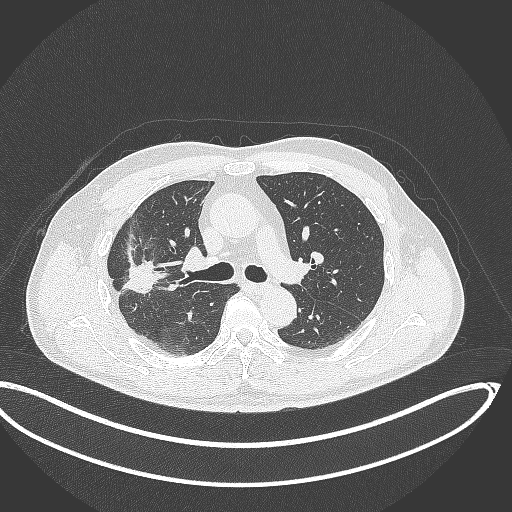
Chest CT, one axial slice. Position 217 of 391 along the scan axis. 120 kVp. Lung window (W 1500 / L -600 HU). 1 mm slice thickness. 512 × 512 image matrix, field of view 439 × 439 mm. Patient: male, 63 years. From the clinical record (not read from this slice): clinical TNM (as recorded): T1c N0 M0; histopathological grade: G2-3.
Structures marked on this image (rectangle marked by the reading radiologist):
- lung tumour (recorded histology: adenocarcinoma): bounding box [x1, y1, x2, y2] px = [122, 255, 162, 300]